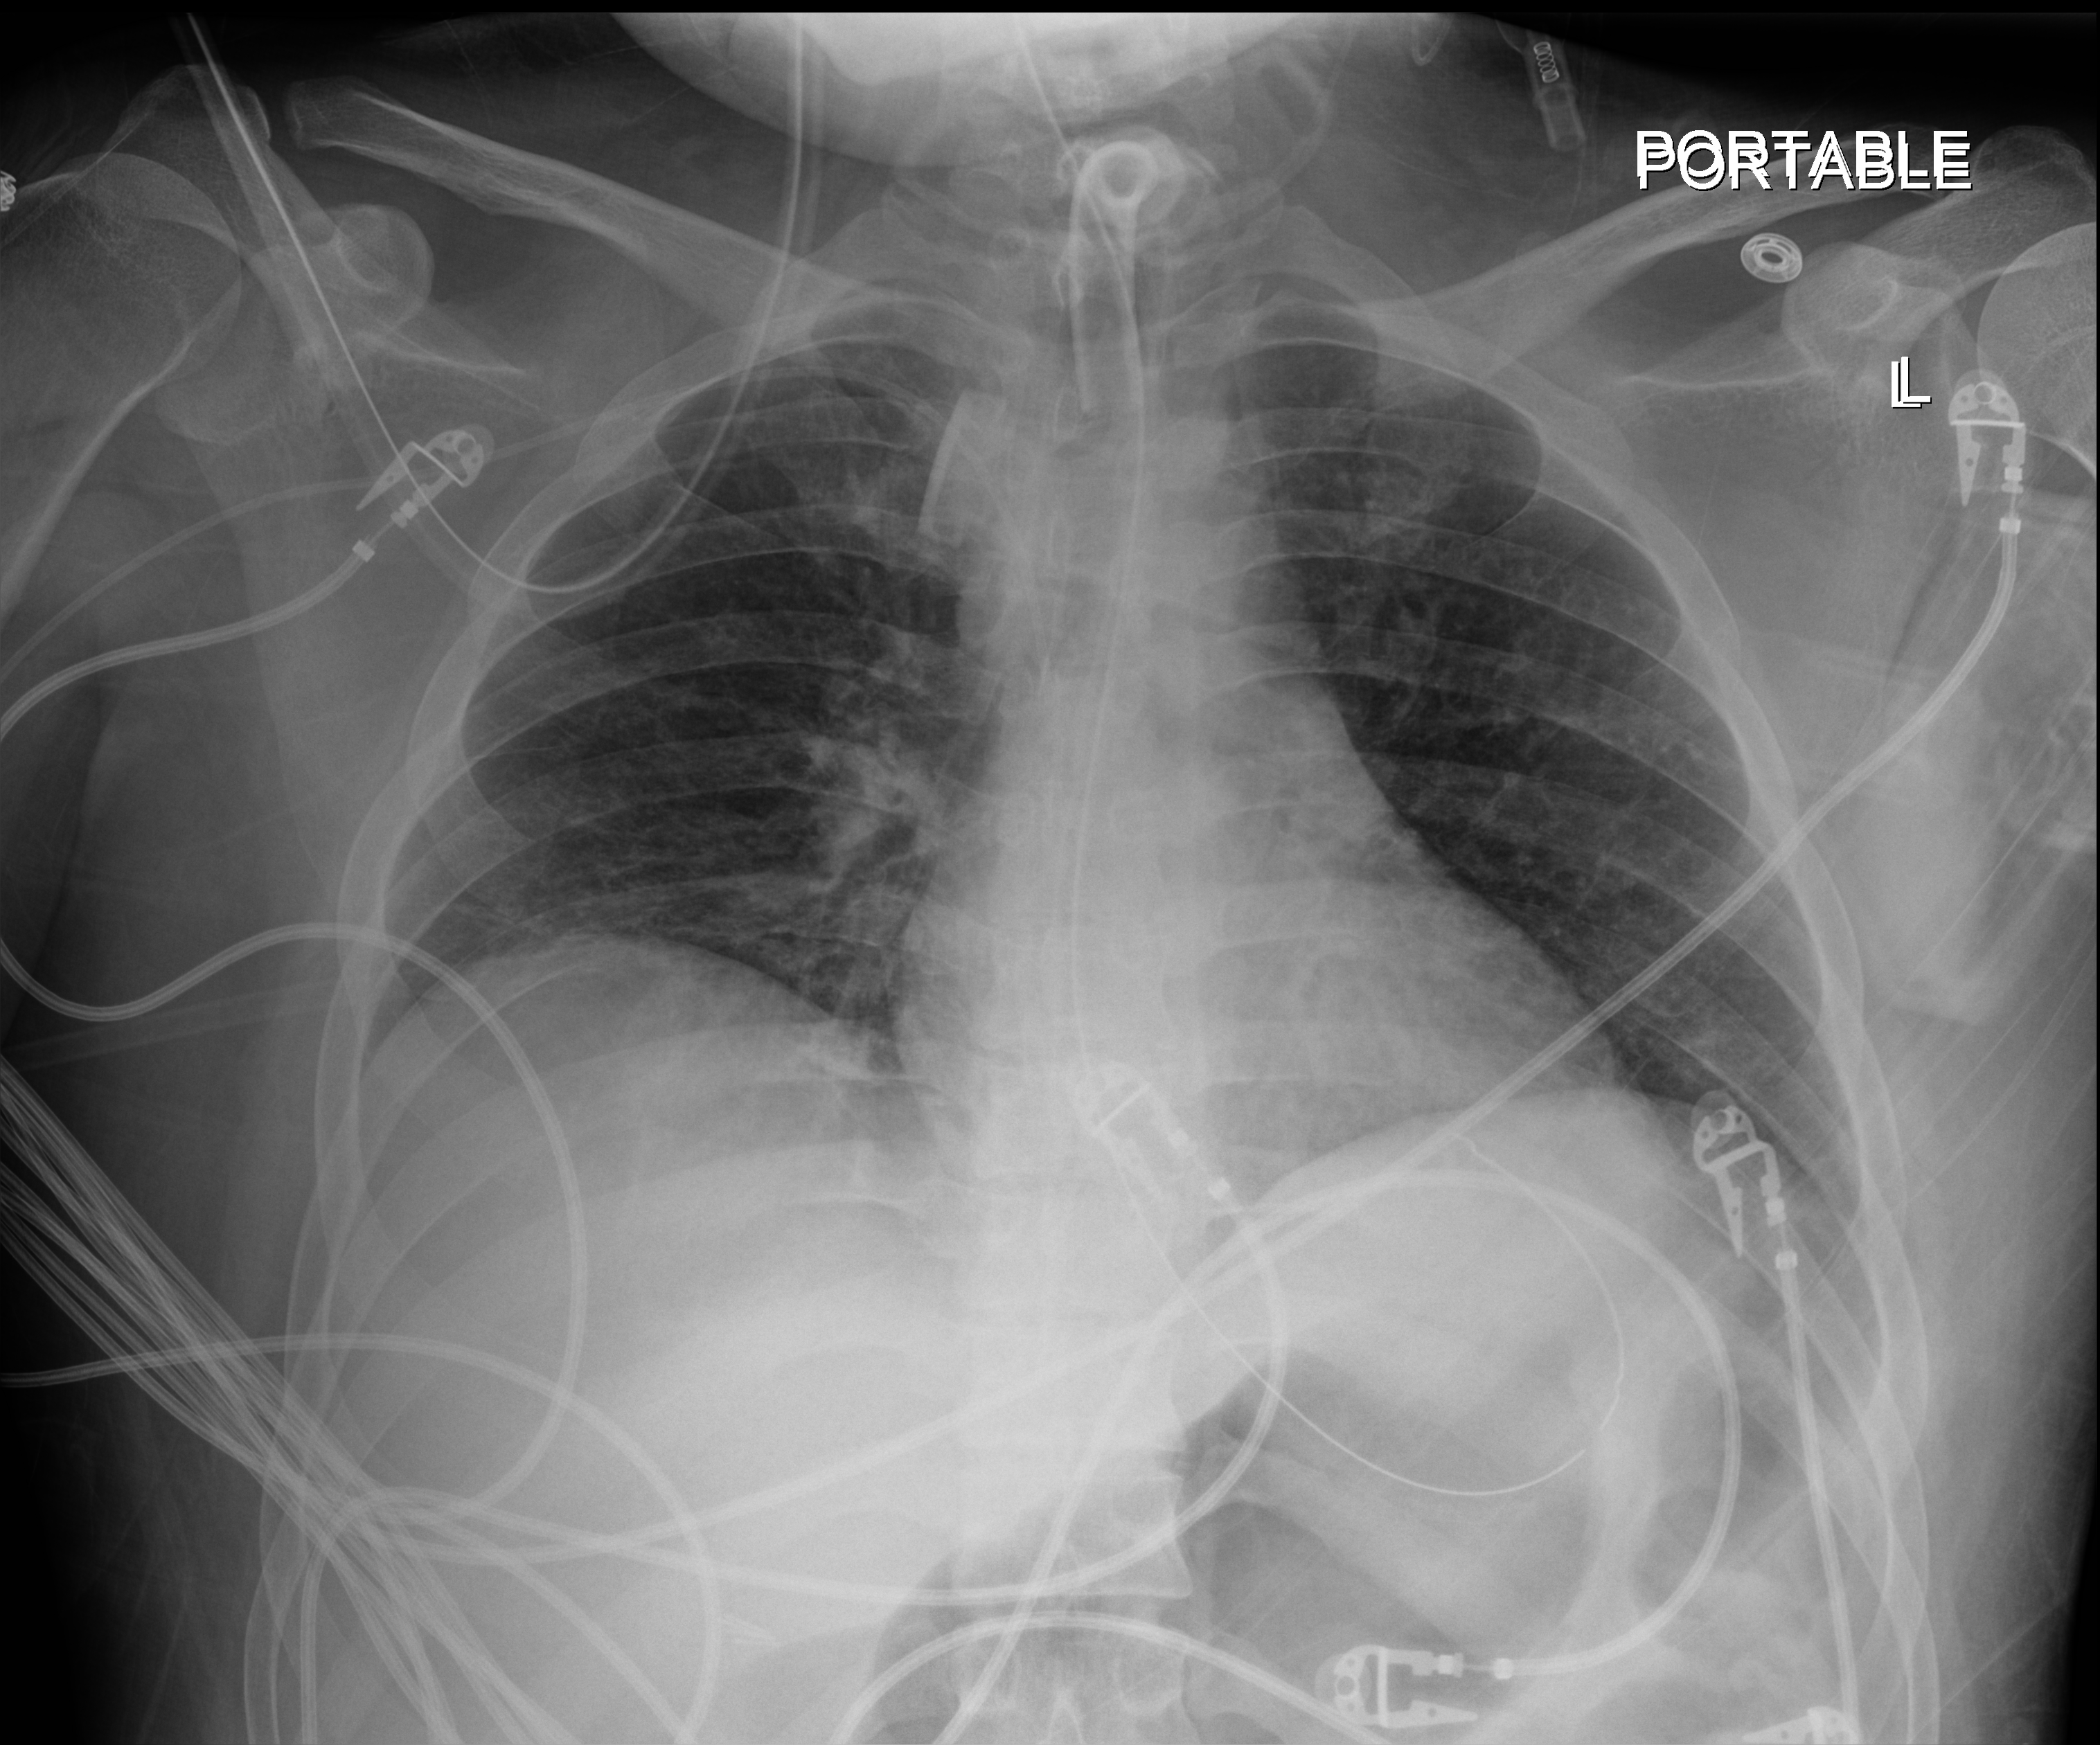
Chest X-ray, anteroposterior (AP) projection. Male patient hospitalised with COVID-19, age 18–59 years.
From the hospital-stay record, not from the radiograph (when in the stay this image was taken is not recorded): admitted to intensive care during this hospital stay: yes; smoking status (admission record): former; chronic kidney disease (admission record): no.